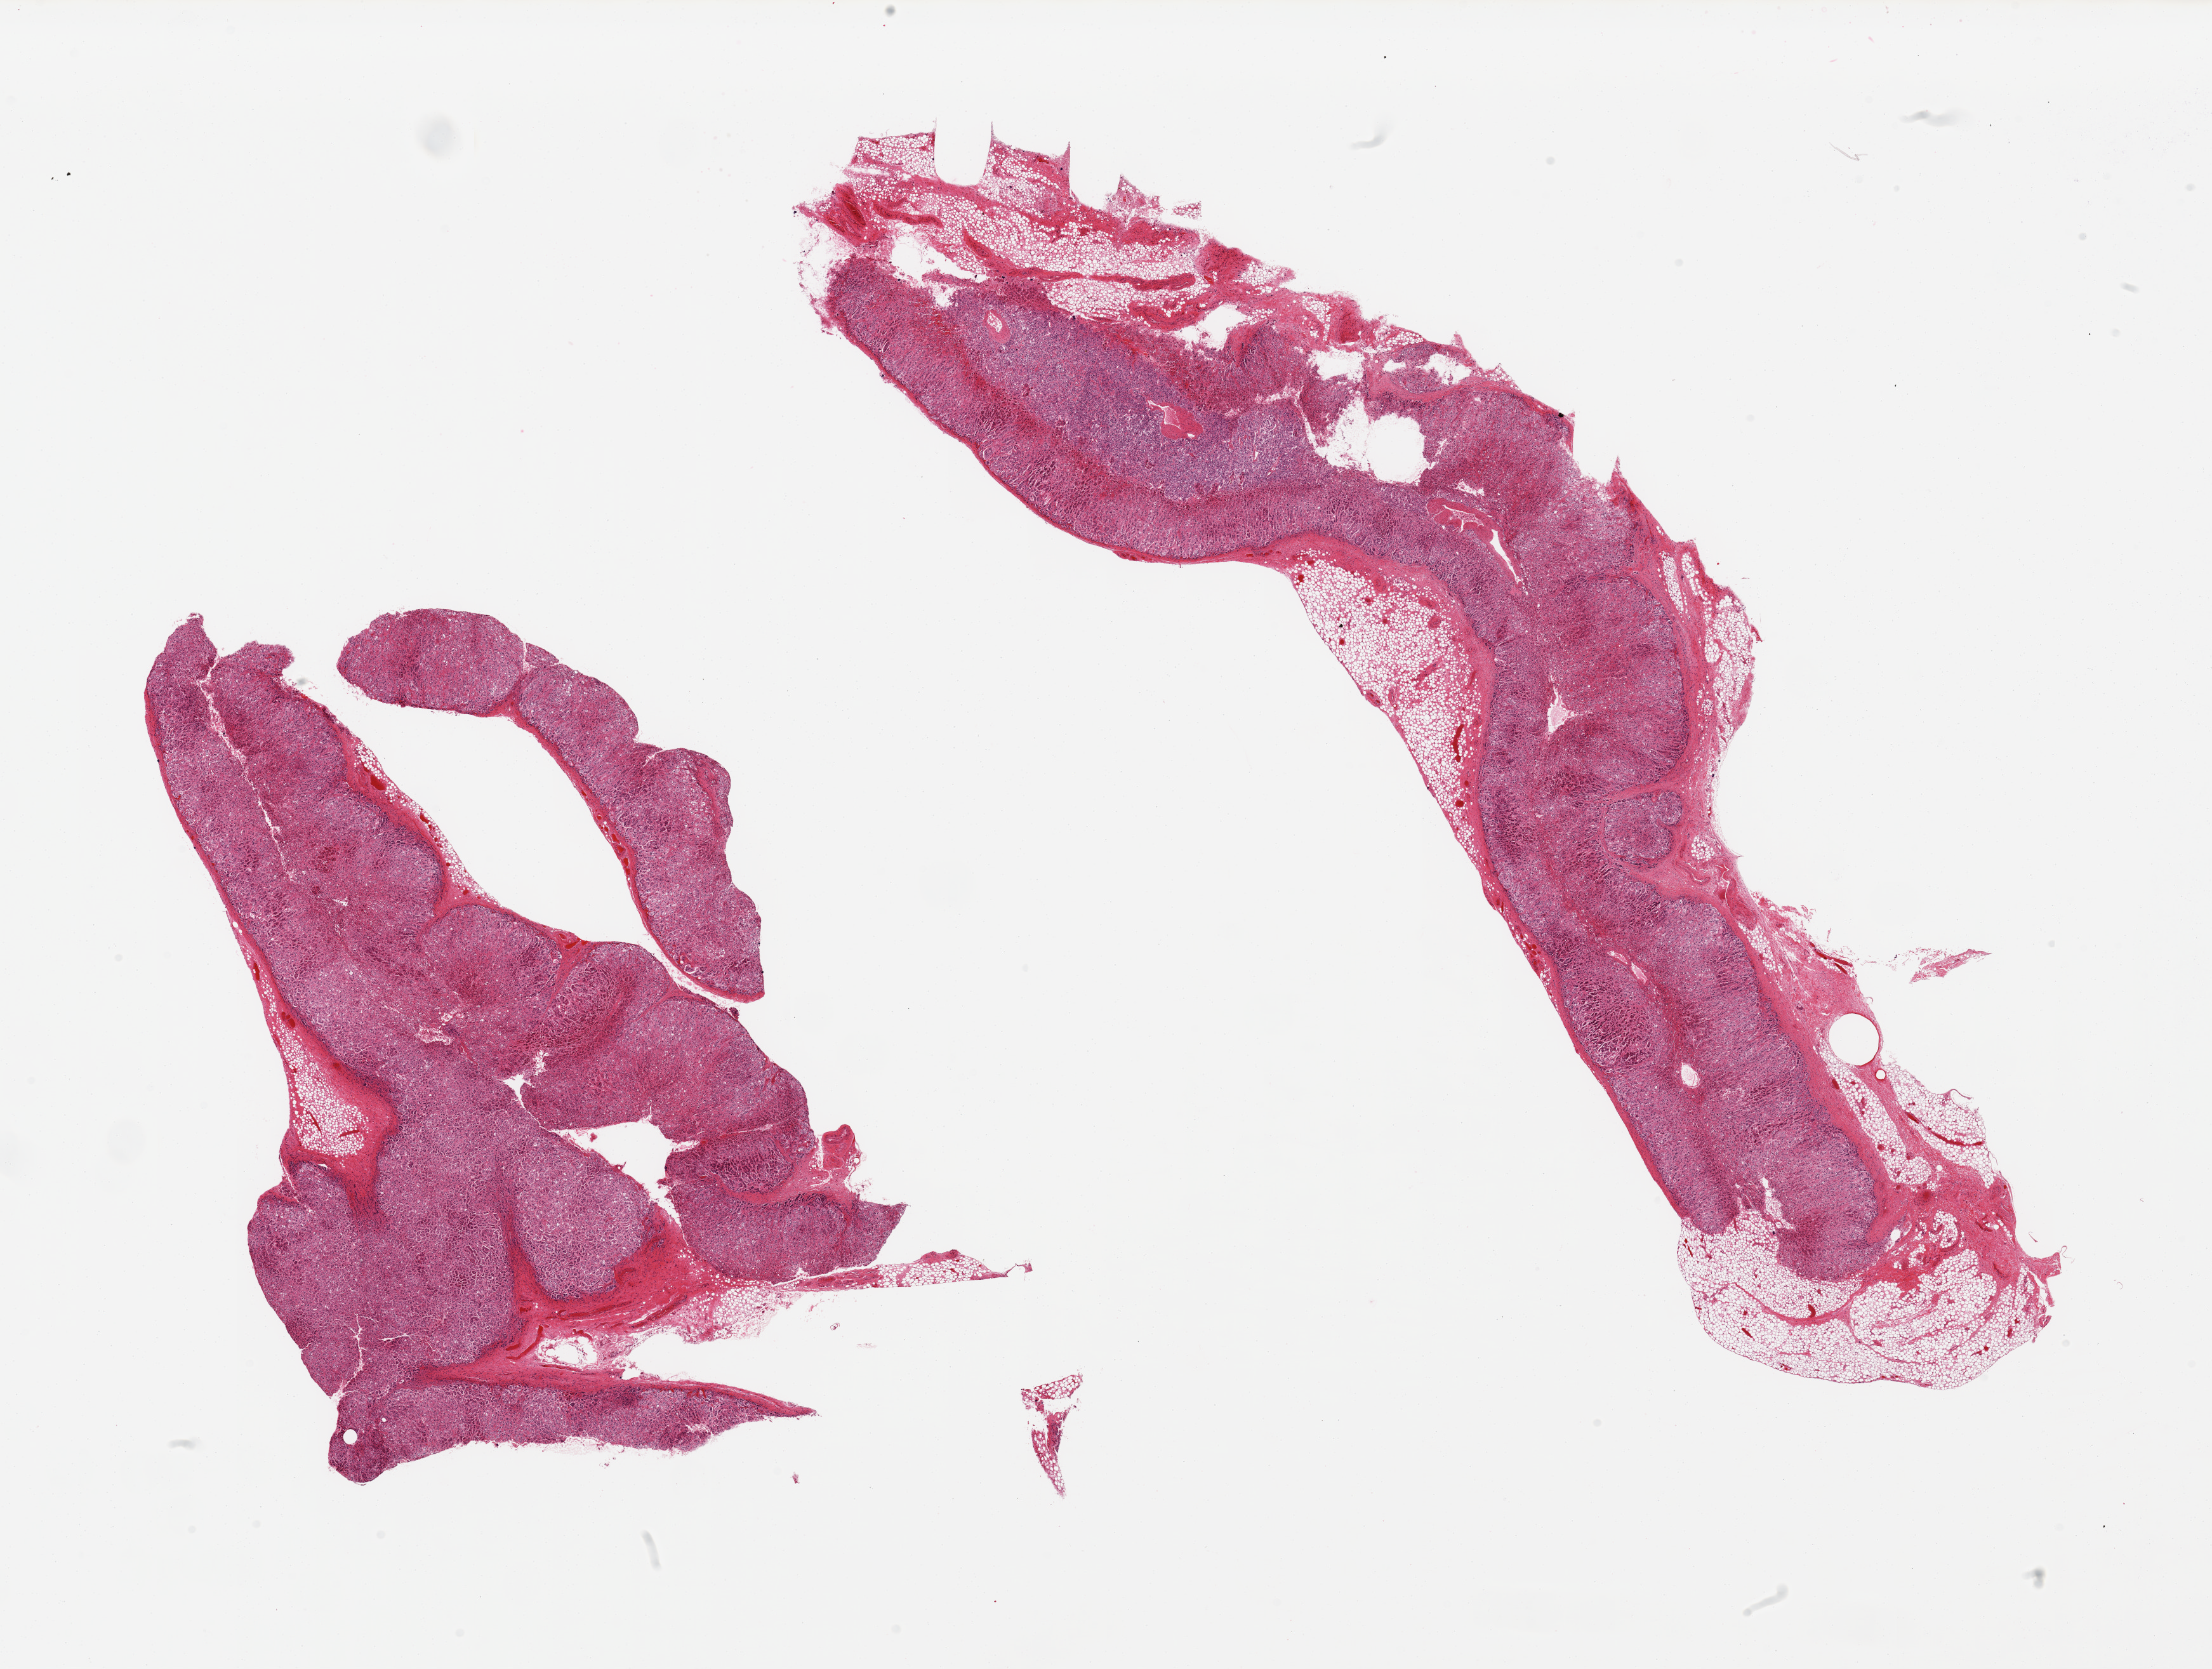
Hematoxylin and eosin (H&E) whole-slide image, brightfield, whole scanned area (about 27.6 x 20.8 mm, from a 20x scan) shown as a low-resolution overview. PAXgene-fixed, paraffin-embedded tissue. Section of adrenal gland (target tissue). Donor tissue sample. Male donor.
Reviewer comment on this tissue sample: 2 pieces; cortex and medulla, one piece has ~30% attached fat.